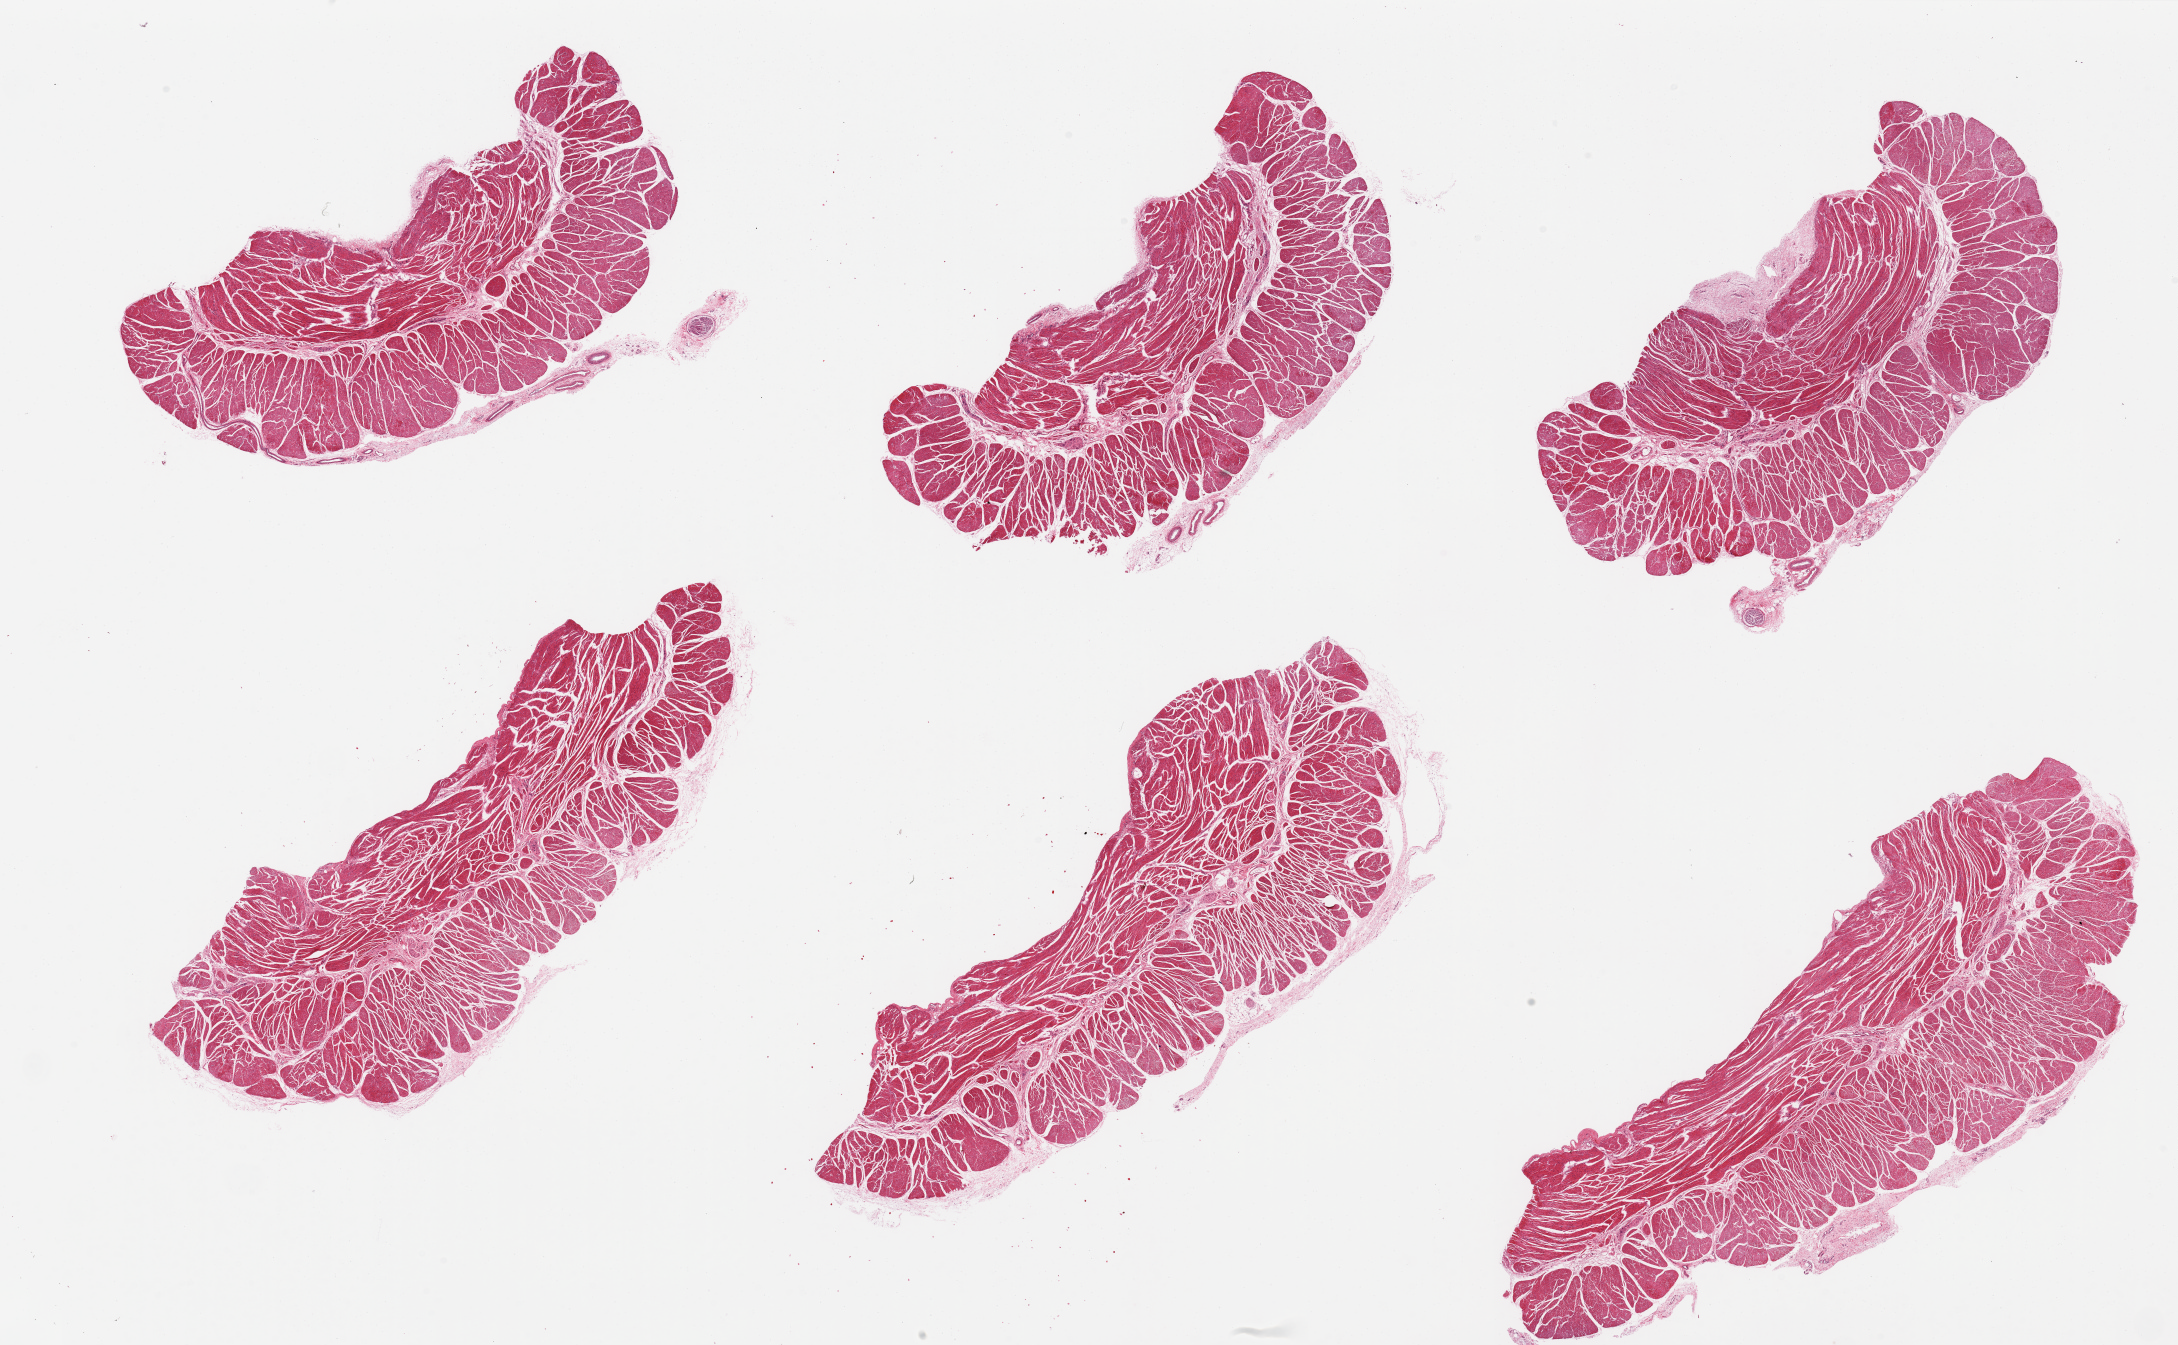
Whole-slide image, hematoxylin and eosin (H&E) stain, low-resolution overview of the scanned area, about 34.5 x 21.3 mm (slide scanned at 20x), PAXgene-fixed, paraffin-embedded tissue, sampled site (target tissue): esophageal muscle, tissue donor sample. Female donor.
Reviewer comment on this tissue sample: 6 pieces, well trimmed.